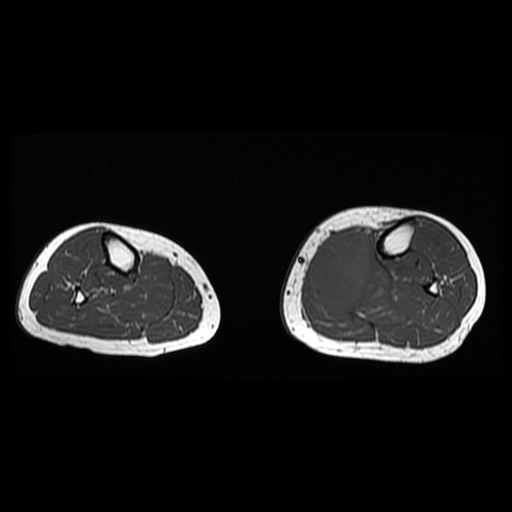
MRI of an extremity soft-tissue mass, one axial slice; slice 12 of 38 in the series (ordered by position); 6 mm slice thickness; 512 × 512 image matrix, field of view 330 × 330 mm. Female patient. From the clinical record (not read from this slice): histological type: extraskeletal high grade osteogenic sarcoma; grade: high; site of the primary tumour: left calf.
Outlined on this slice (manually delineated by an expert):
- gross tumour volume (mass): bounding box [x1, y1, x2, y2] px = [313, 230, 371, 309]